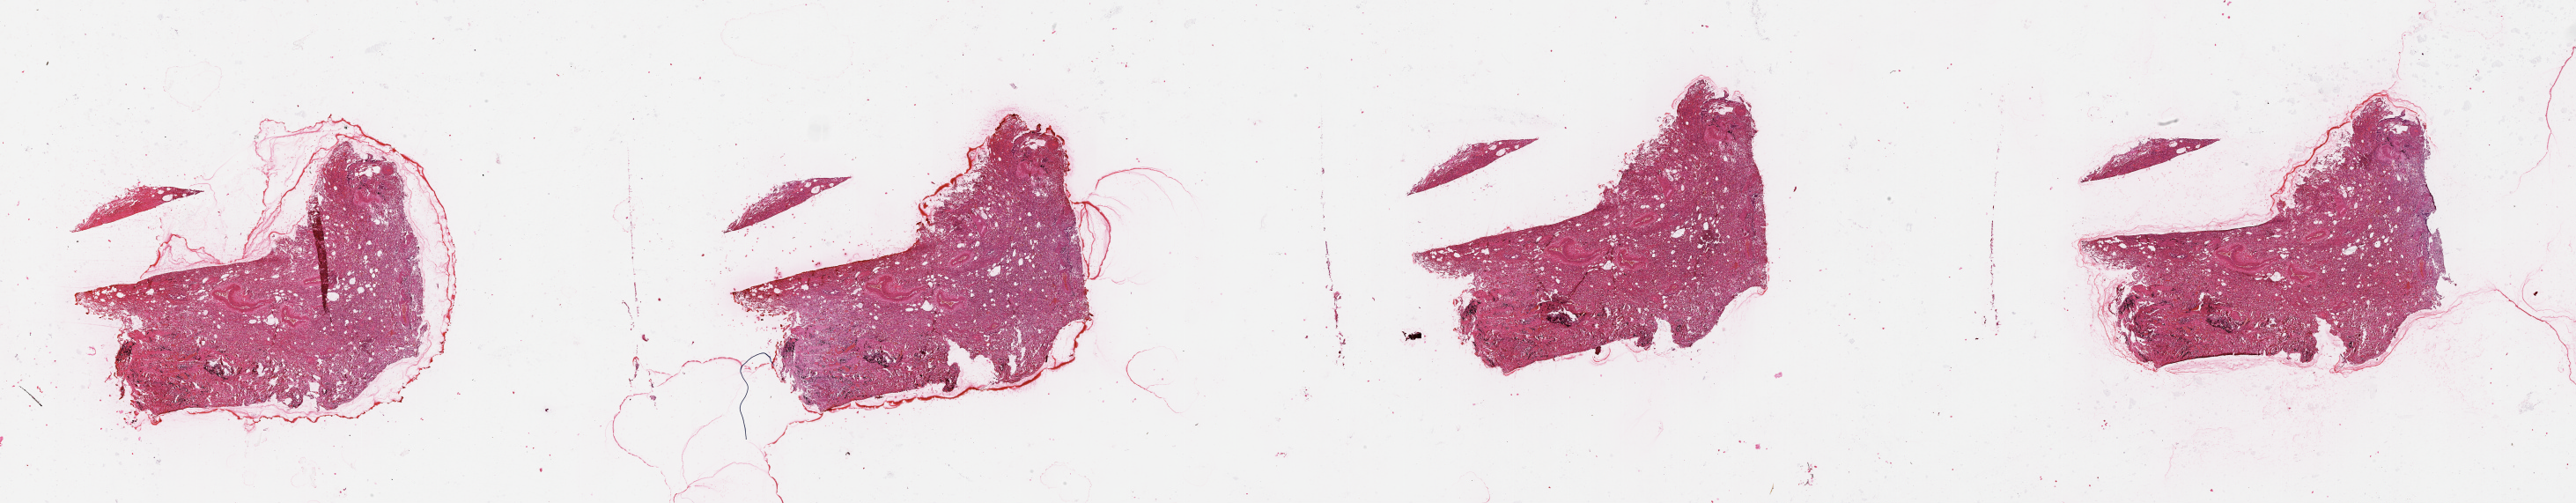
Whole-slide histology image, H&E — whole scanned area (about 47.1 x 9.2 mm) shown as a low-resolution overview; lung, tissue type not recorded.
Patient diagnosis (cohort enrolment): squamous cell carcinoma (lung).